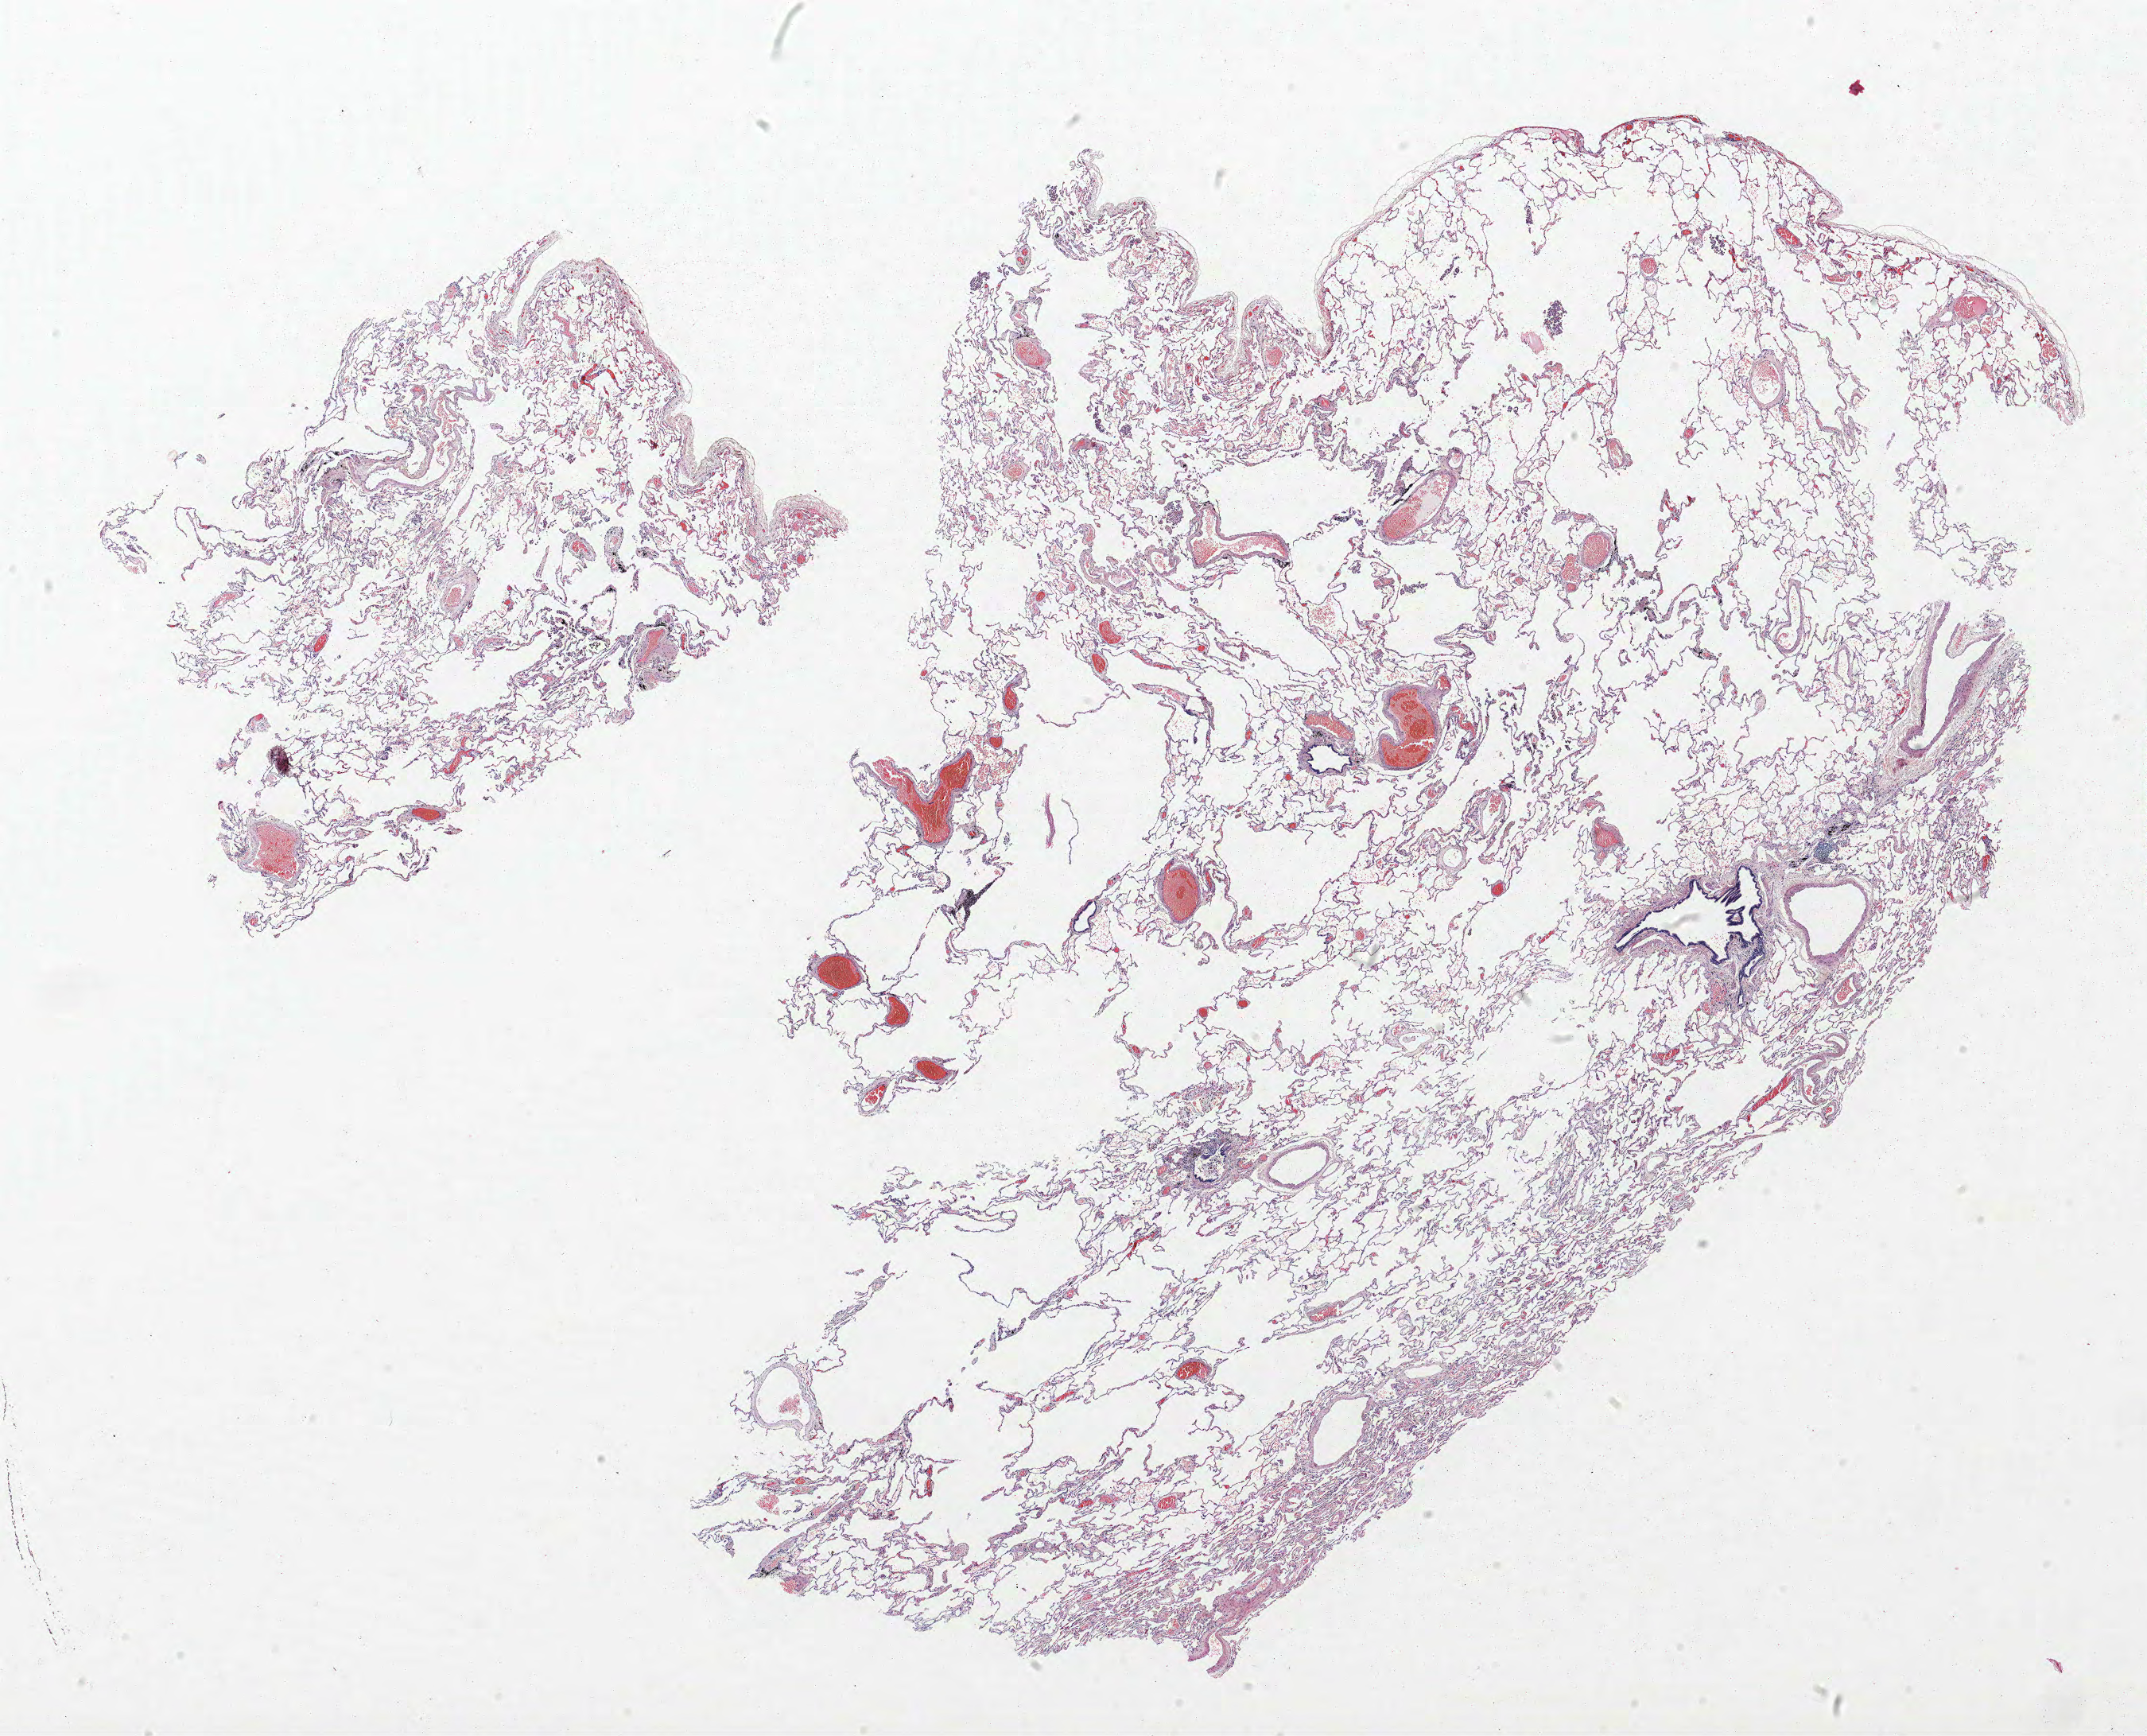
Whole-slide histology image, H&E-stained — low-resolution overview of the scanned area, about 21.6 x 17.5 mm (slide scanned at 40x). Formalin-fixed paraffin-embedded (FFPE) section. Lung. Male patient, aged 70 at enrolment. Current smoker at enrolment. Grade: poorly differentiated (G3).
* primary tumour location (clinical record): right lower lobe
* tumour size (pathology): 24 mm
* stage (AJCC 6th edition): IB
* participant's lung-cancer diagnosis: Squamous cell carcinoma, NOS